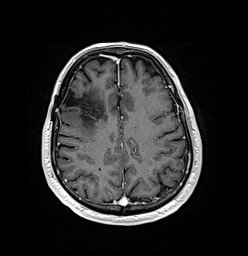
Brain MRI from a brain-tumour surgery series, one axial slice; slice 53 of 176 in the series (ordered by position); T1-weighted post-contrast; 248 × 256 image matrix, field of view 242 × 250 mm. From the clinical record (not read from this slice): histopathology: Oligodendroglioma; WHO grade: 3; IDH mutation: yes; tumour location: Right Frontal.
Structures marked on this image (expert manual segmentation):
- previous resection cavity: bounding box (x1, y1, x2, y2) in pixels: (63, 90, 84, 107)